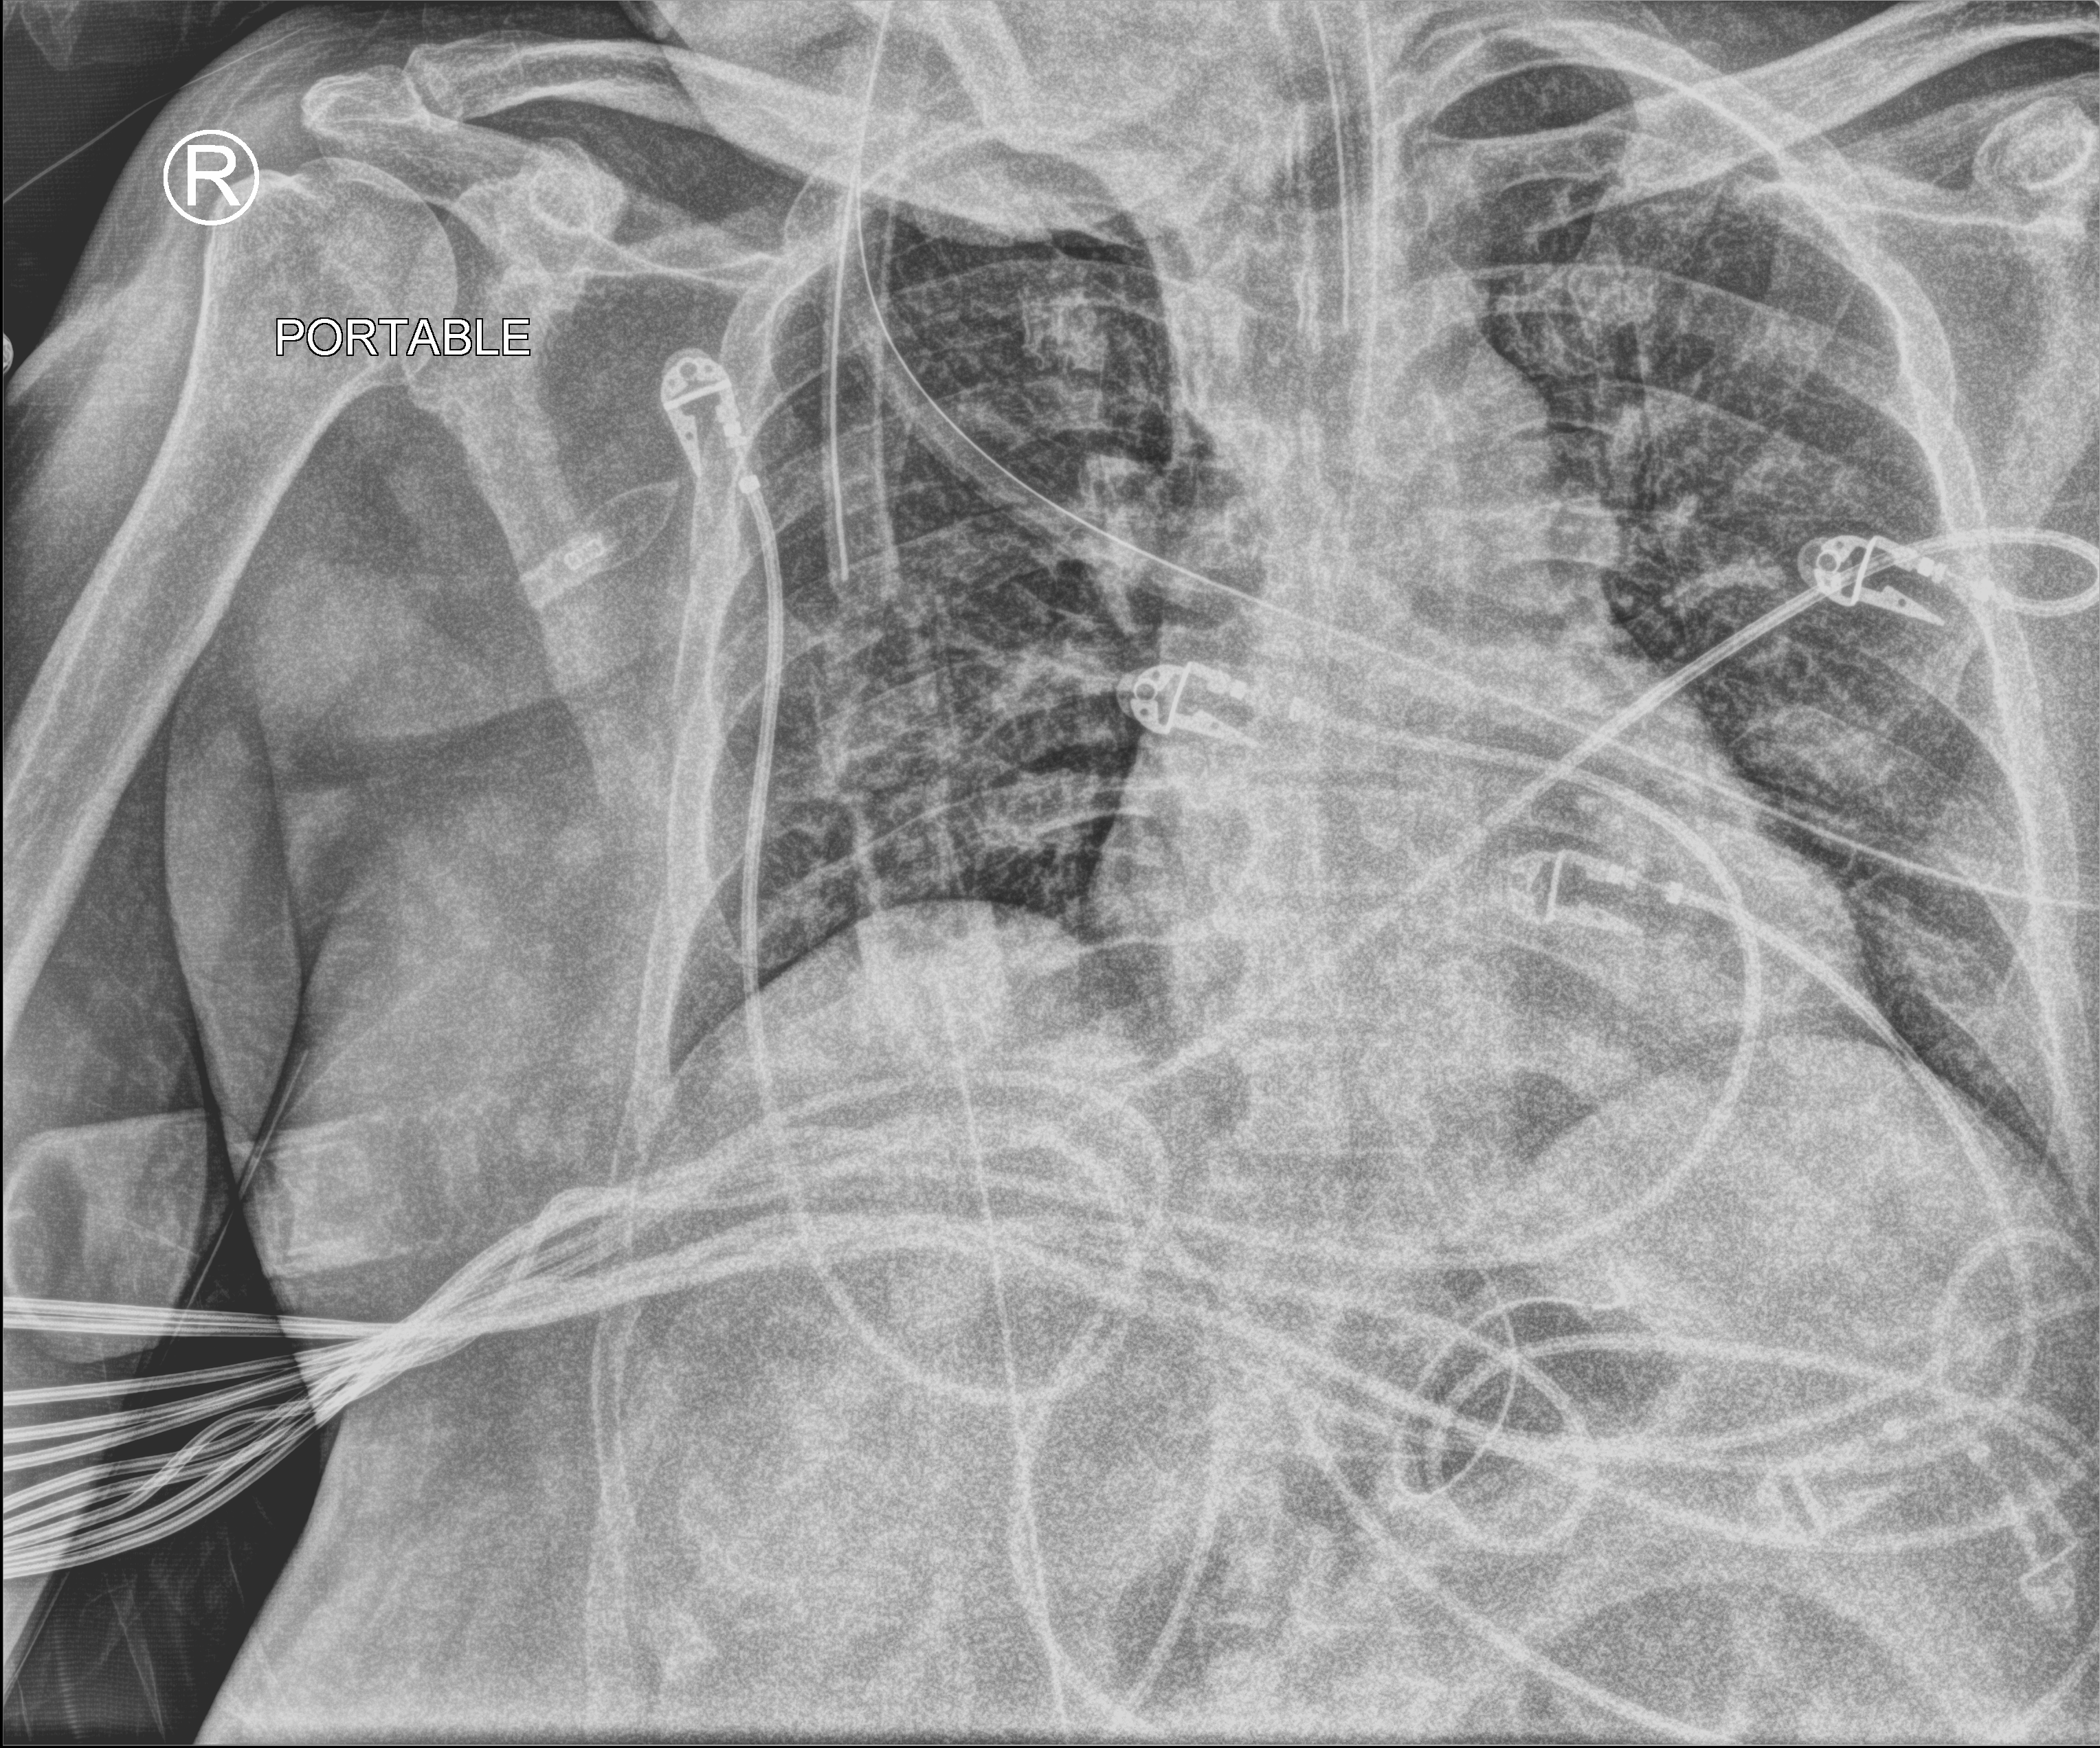
Bedside chest radiograph (computed radiography). Adult patient hospitalised with COVID-19, age 18–59 years.
From the hospital-stay record, not from the radiograph (when in the stay this image was taken is not recorded): hypertension (admission record): no; admitted to intensive care during this hospital stay: yes.